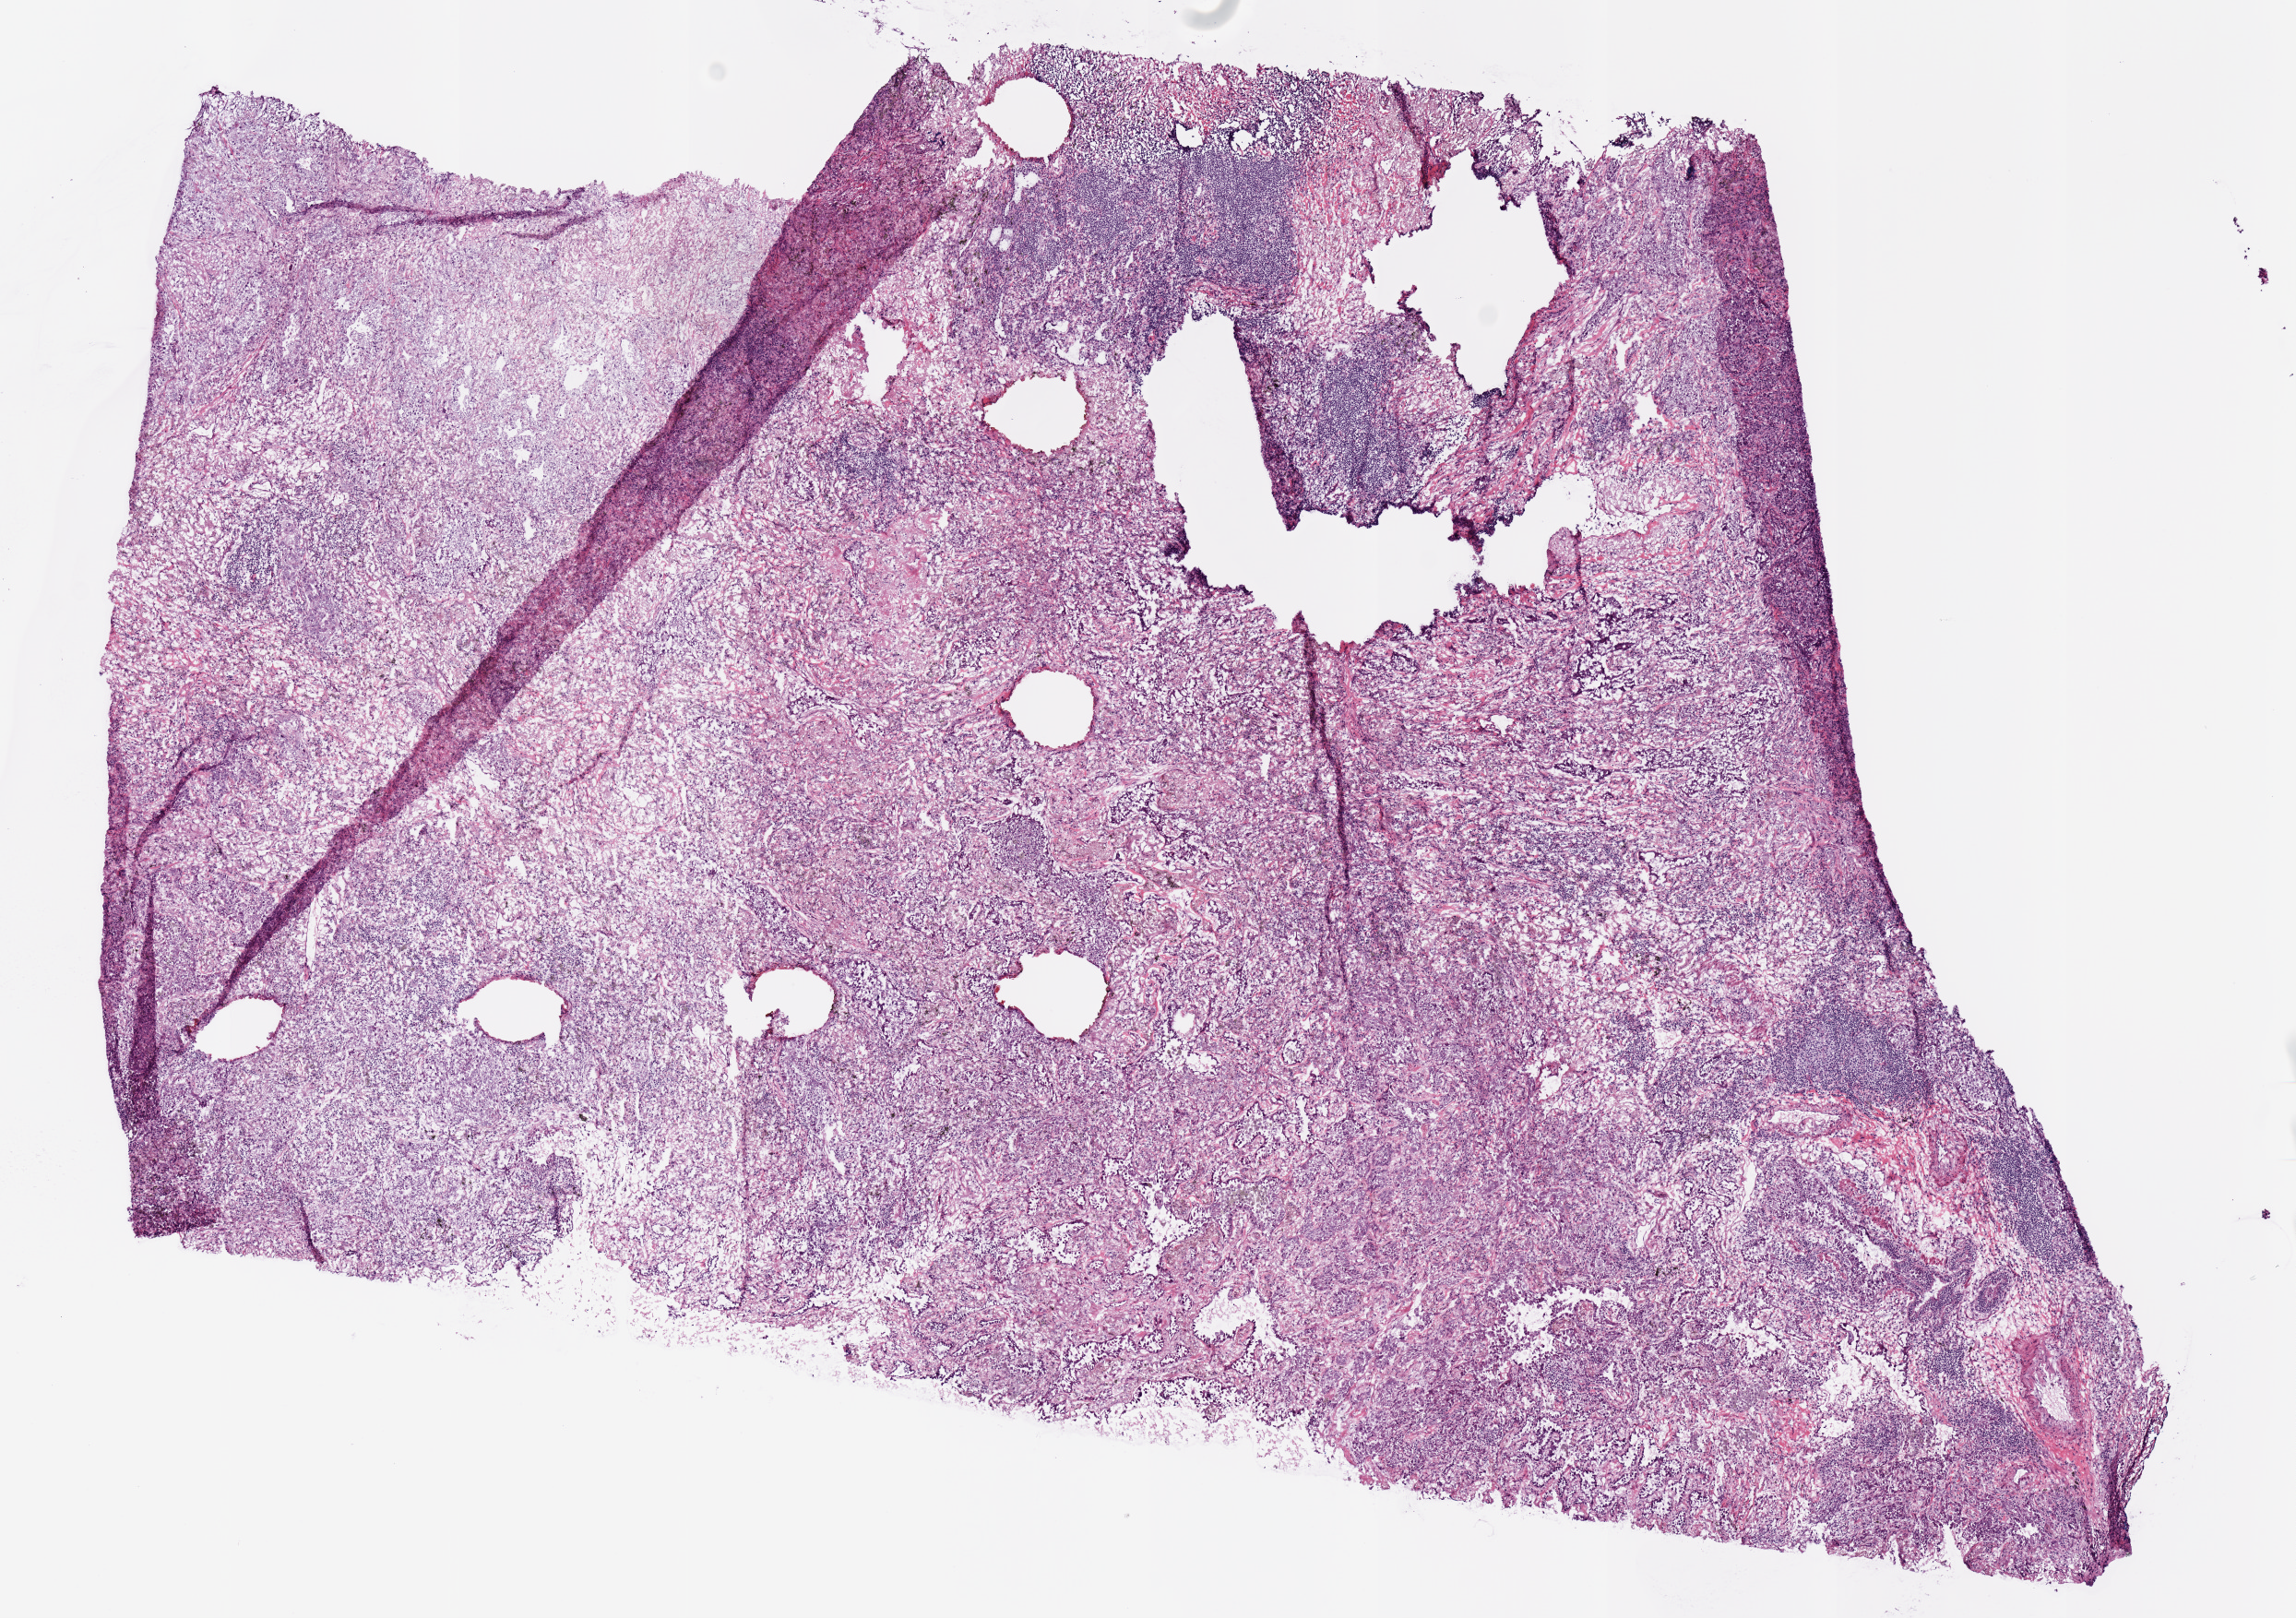
Digitized H&E tissue section (whole slide) — shown as a low-resolution overview of the whole scanned area (about 9.8 x 6.9 mm, slide scanned at 20x), frozen section from the top of the tissue portion, primary tumour sample from the lung. Male, age 54 years at initial diagnosis. Composition of this section per pathologist review: tumour cells 70%, tumour nuclei 60%, normal cells 0%, stromal cells 30%, necrosis 0%.
* AJCC pathologic stage: IB (7th edition)
* TNM: T2a N0 M0
* histologic diagnosis: Adenocarcinoma, NOS (upper lobe, lung)